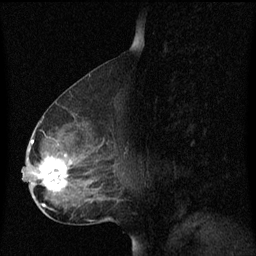
Breast MRI (dynamic contrast-enhanced), one sagittal slice. Position 37 of 60 along the scan axis. Dynamic contrast-enhanced series, image 2 of 3 at this slice position (ordered by acquisition). 1.5 T. TE 4.2 ms, TR 8.4 ms. 256 × 256 image matrix, field of view 200 × 200 mm. Patient: female, 49 years. Case-level facts recorded for this patient, not image findings: setting: breast cancer imaged before/during neoadjuvant chemotherapy; receptor status: HR-positive, HER2-negative.
Annotated regions visible in this slice (semi-automatic segmentation, software-assisted and operator-edited):
- analysis volume of interest (the breast-tissue region the enhancement analysis was run in; not a lesion): bounding box (x1, y1, x2, y2) in pixels: (22, 126, 115, 201)
- tumour enhancement mask (voxels above the 70 % enhancement threshold inside the analysis volume of interest): (32, 140, 78, 193)